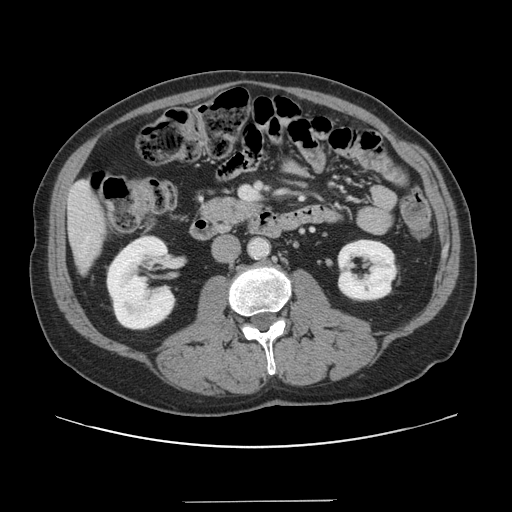
Contrast-enhanced abdominal CT, one axial slice. Slice 44 of 151 in the series (ordered by position). Intravenous contrast given. Soft-tissue window (W 400 / L 40 HU). 512 × 512 image matrix, field of view 399 × 399 mm. Male patient, age 63 years. From the clinical record (not read from this slice): diagnosis: colorectal cancer liver metastases, imaged before liver resection; multiple liver metastases: no; largest metastasis: 2.1 cm; disease in both lobes: no.
Structures marked on this image (outlined manually by an expert reader):
- liver: bounding box <69,183,105,269> (left, top, right, bottom; pixels)
- planned liver remnant (the part of the liver to remain after resection): <69,183,105,269>
- portal vein (with intrahepatic branches): <242,187,253,199>